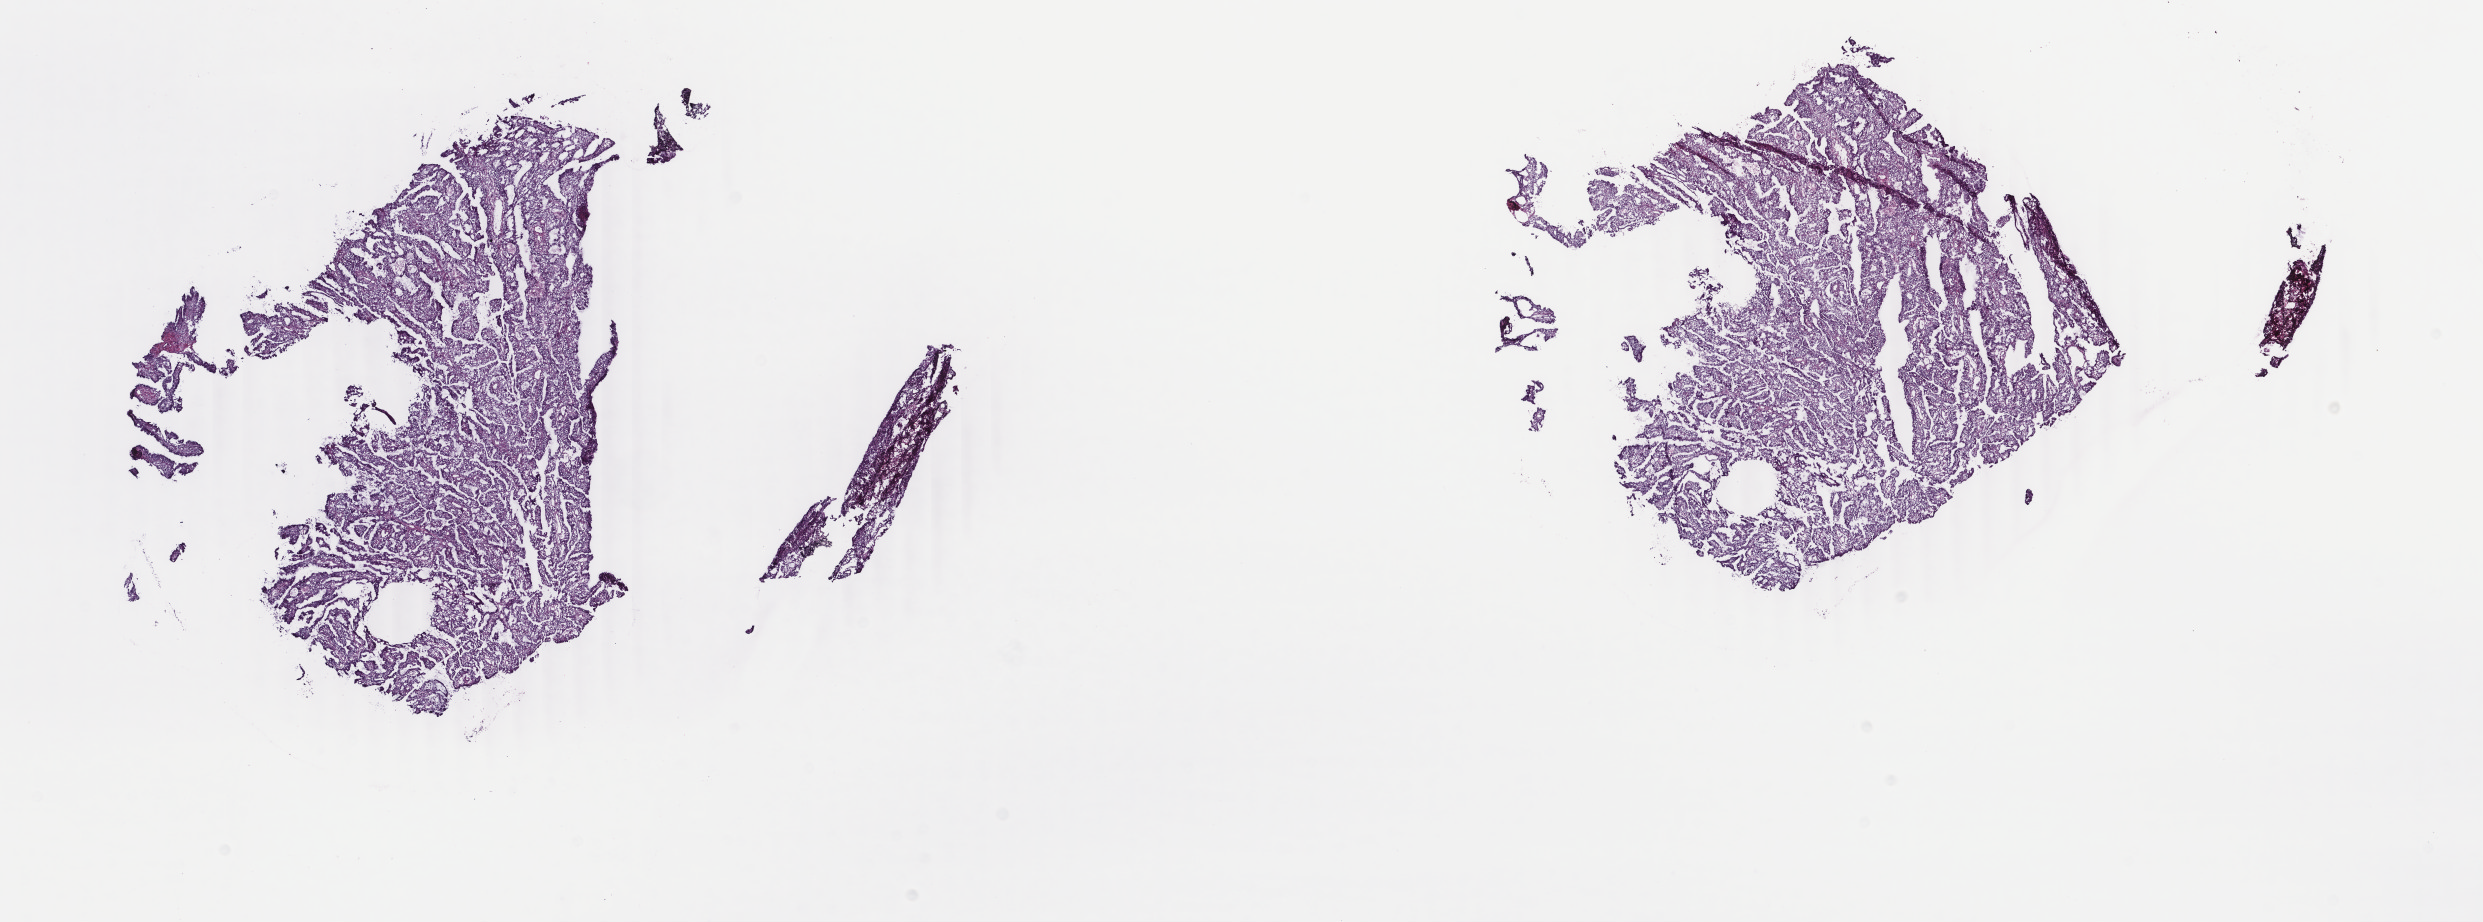
Digitized H&E tissue section (whole slide) — whole scanned area (about 19.8 x 7.3 mm, from a 40x scan) shown as a low-resolution overview. Frozen section from the top of the tissue portion. Uterus, primary tumour sample. Female, age 59 years at initial diagnosis. Histologic grade: G3 (poorly differentiated). Composition of this section per pathologist review: tumour cells 80%, tumour nuclei 80%, normal cells 0%, stromal cells 10%, necrosis 10%. Inflammatory infiltration, as recorded: lymphocyte infiltration 30%, monocyte infiltration 10%, neutrophil infiltration 50%.
Lymph nodes positive (case pathology): 0 of 40 examined. FIGO stage: IIA. Histologic diagnosis: Endometrioid adenocarcinoma, NOS (endometrium).